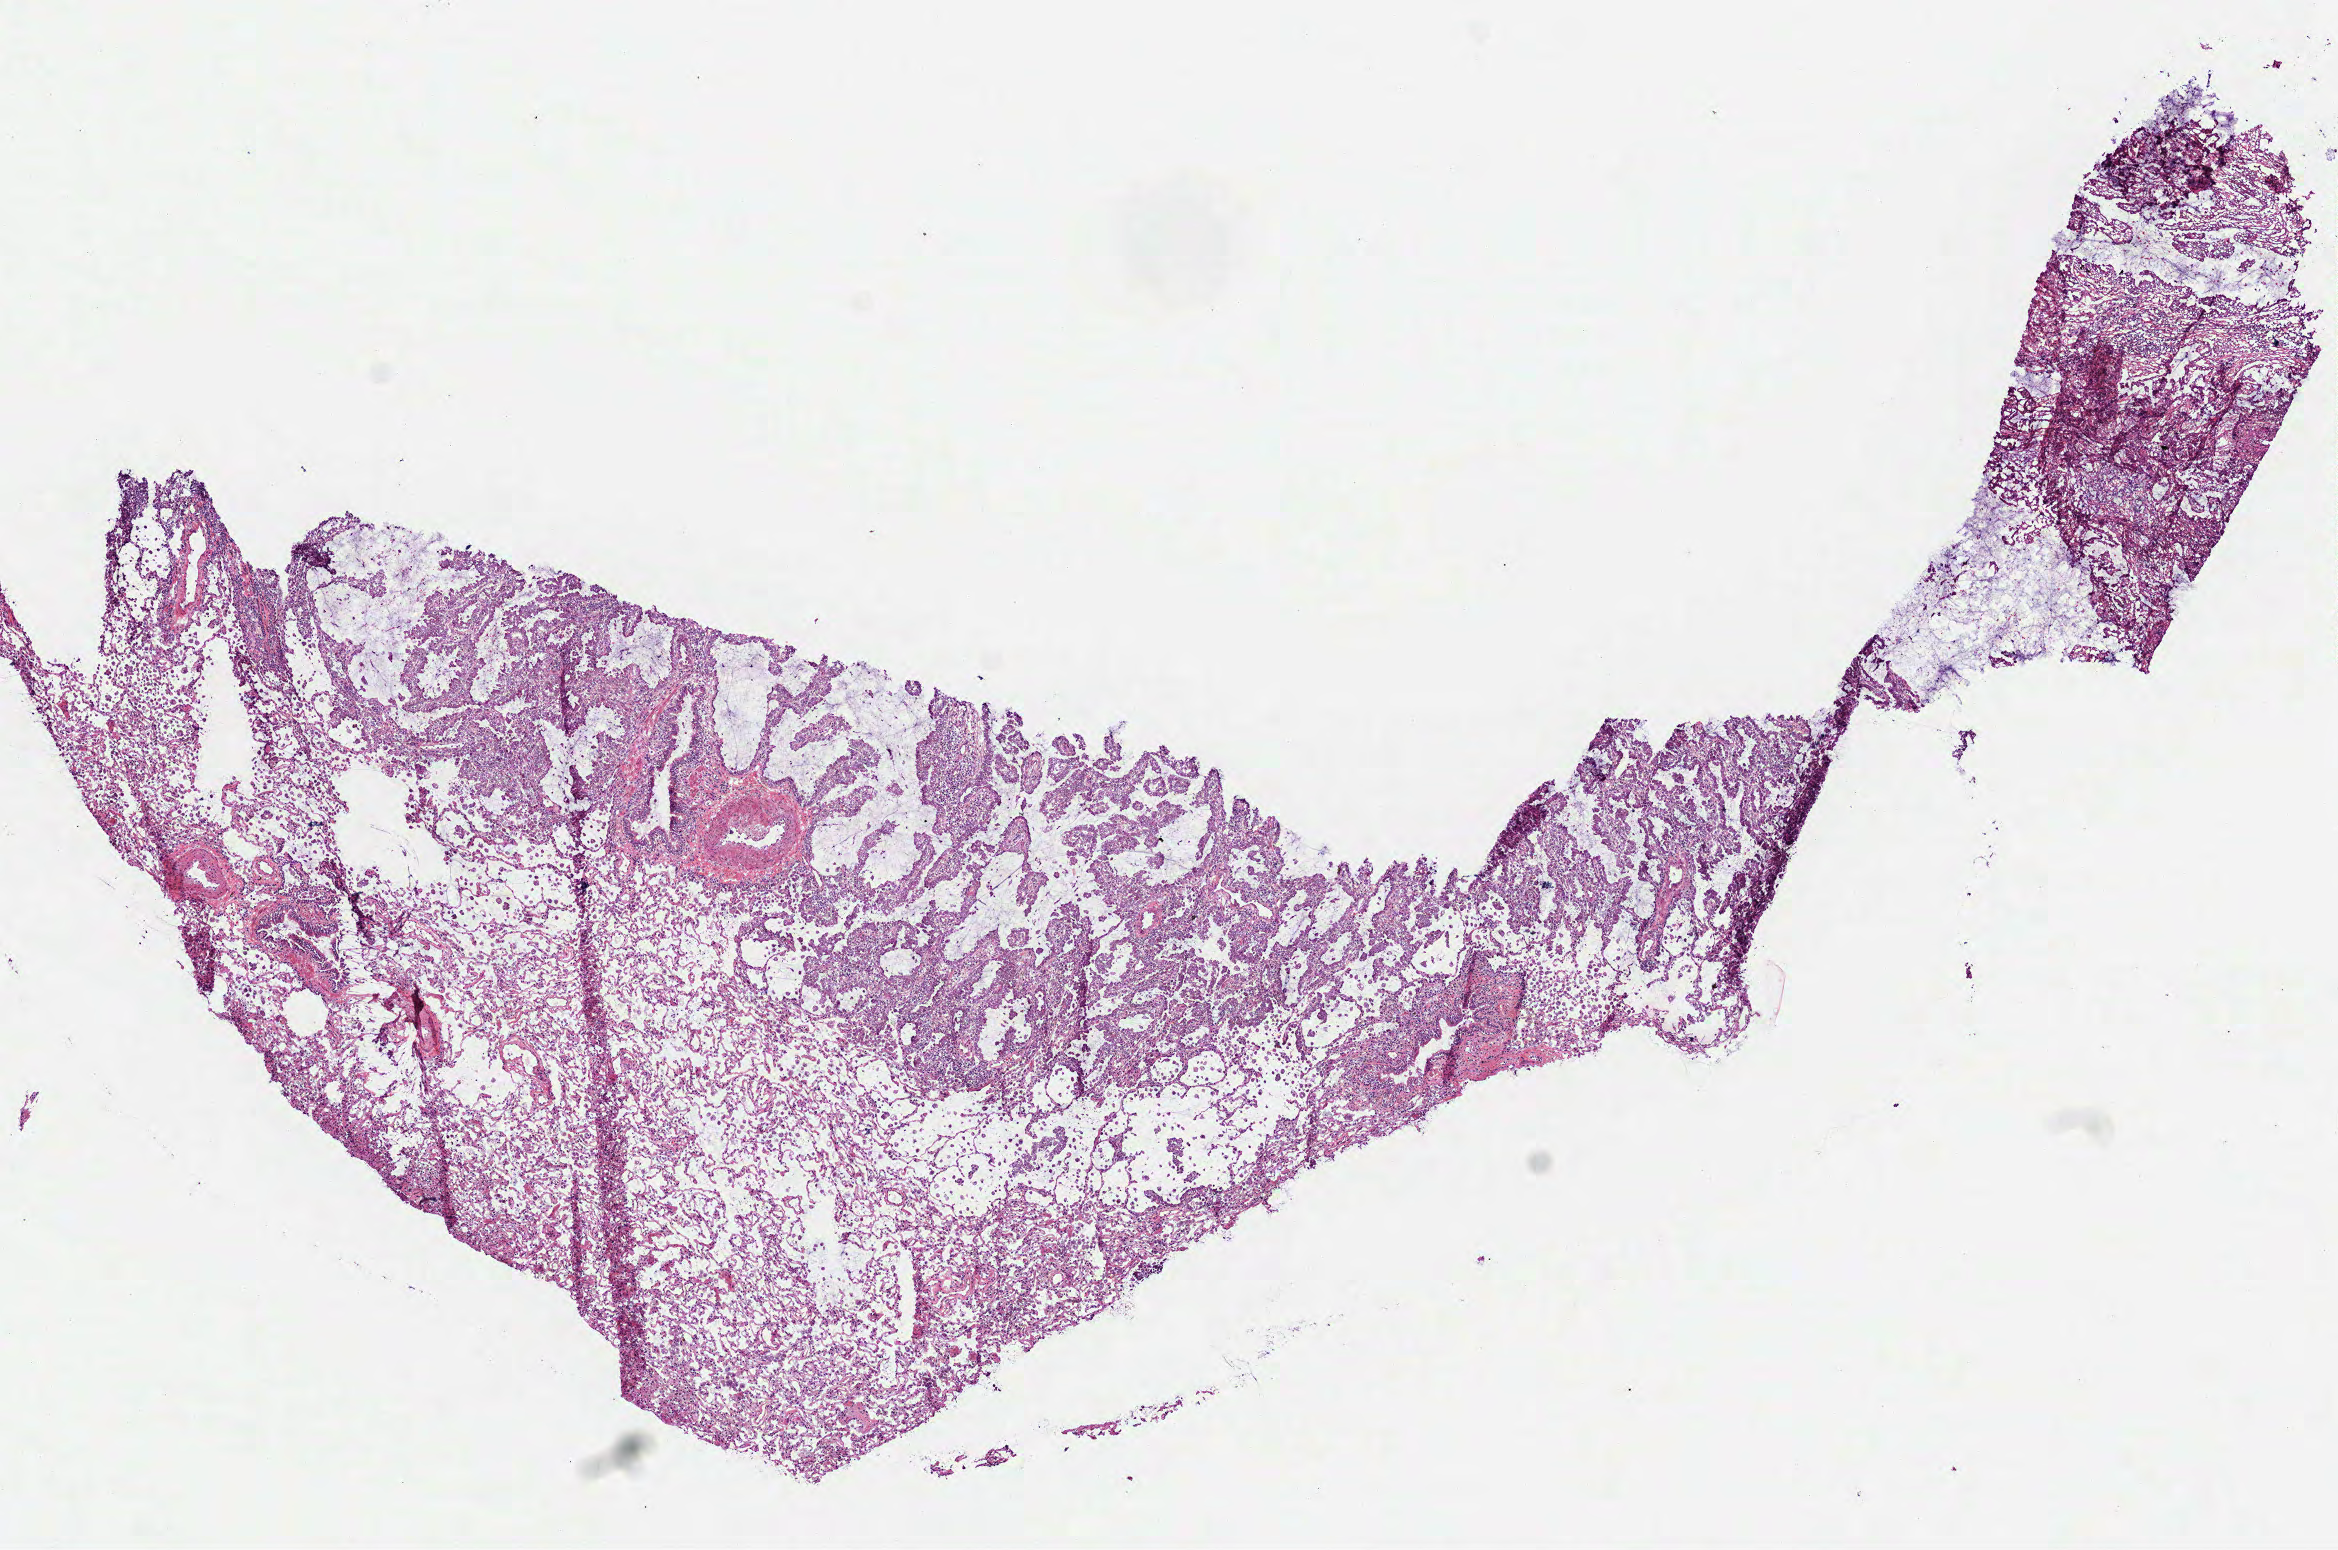
H&E-stained whole-slide image — shown as a low-resolution overview of the whole scanned area (about 9.4 x 6.2 mm, acquisition: 40x scan). Frozen section. Primary tumour sample from the lung. Male patient; age at initial diagnosis 69 years. Pathologist review of this section (percent, as recorded): tumour cells 50%, tumour nuclei 55%, normal cells 50%, stromal cells 0%, necrosis 0%. Inflammatory infiltration, as recorded: lymphocyte infiltration 5%, monocyte infiltration 10%.
• TNM: T1b N0 M0
• histologic diagnosis: Acinar cell carcinoma (middle lobe, lung)
• AJCC pathologic stage: IA (7th edition)